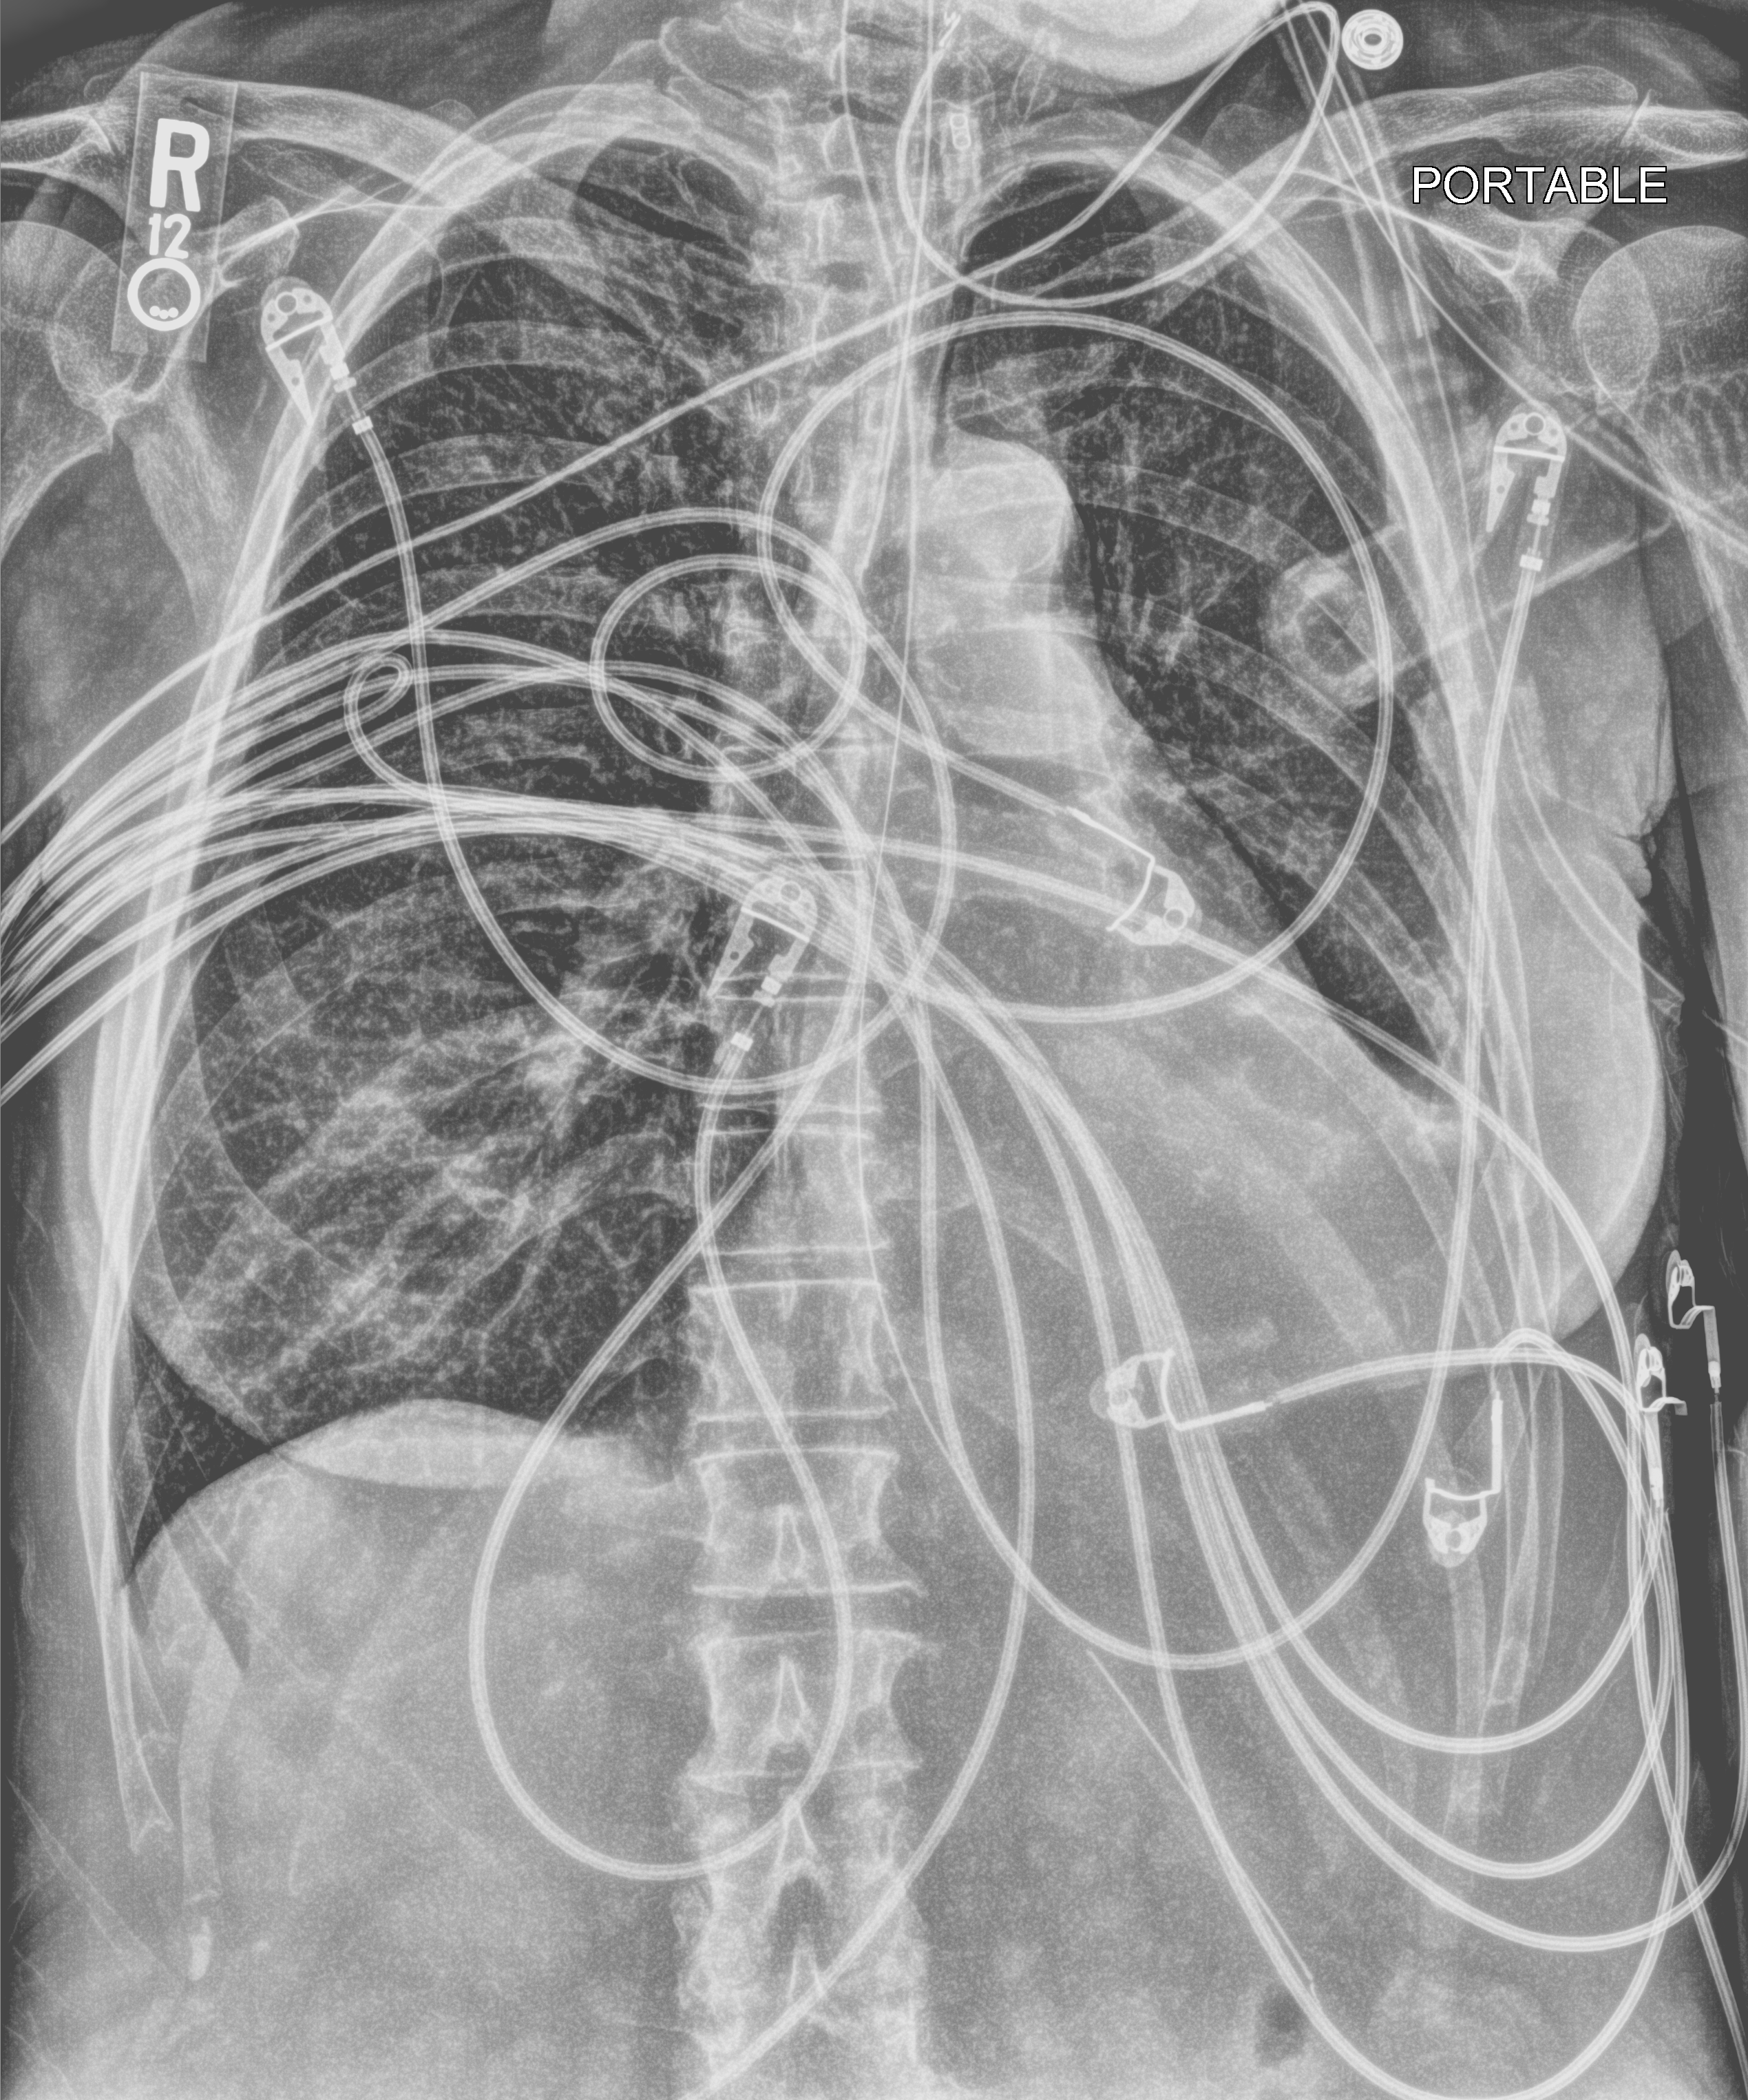
Bedside chest radiograph (computed radiography); anteroposterior (AP) projection. Female patient hospitalised with COVID-19, age 60–74 years.
Admission-level facts for this patient (not findings on this image; timing relative to this image not recorded): length of hospital stay: 38 days; admitted to intensive care during this hospital stay: yes; mechanically ventilated during this hospital stay: yes.